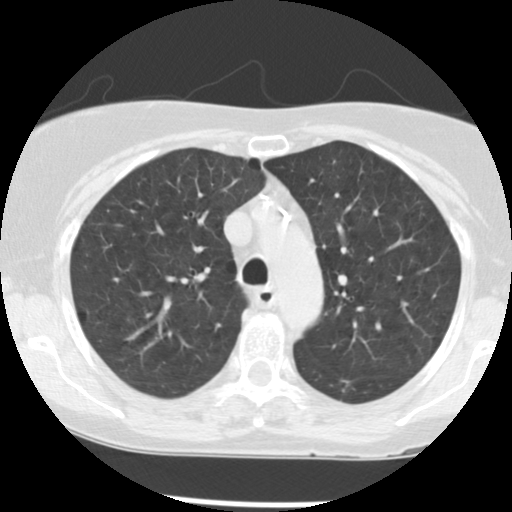
Chest CT (low-dose screening protocol), one axial image; second annual screen; lung window (W 1500 / L -600 HU); 2.5 mm slice thickness; 120 kVp; slice 32 of 124 in the series; 512 × 512 image matrix, field of view 292 × 292 mm. Female participant, aged 63 years at enrolment.
Expert reader's lesion annotation, bounding box (x1, y1, x2, y2) in pixels: (327, 371, 371, 407). Reader record for this screening exam (exam-level; its link to the box is not recorded): non-calcified nodule or mass ≥4 mm, left lower lobe, 7 × 6 mm, poorly defined margins, soft tissue attenuation, pre-existing on the prior screen: yes; interval growth: yes.